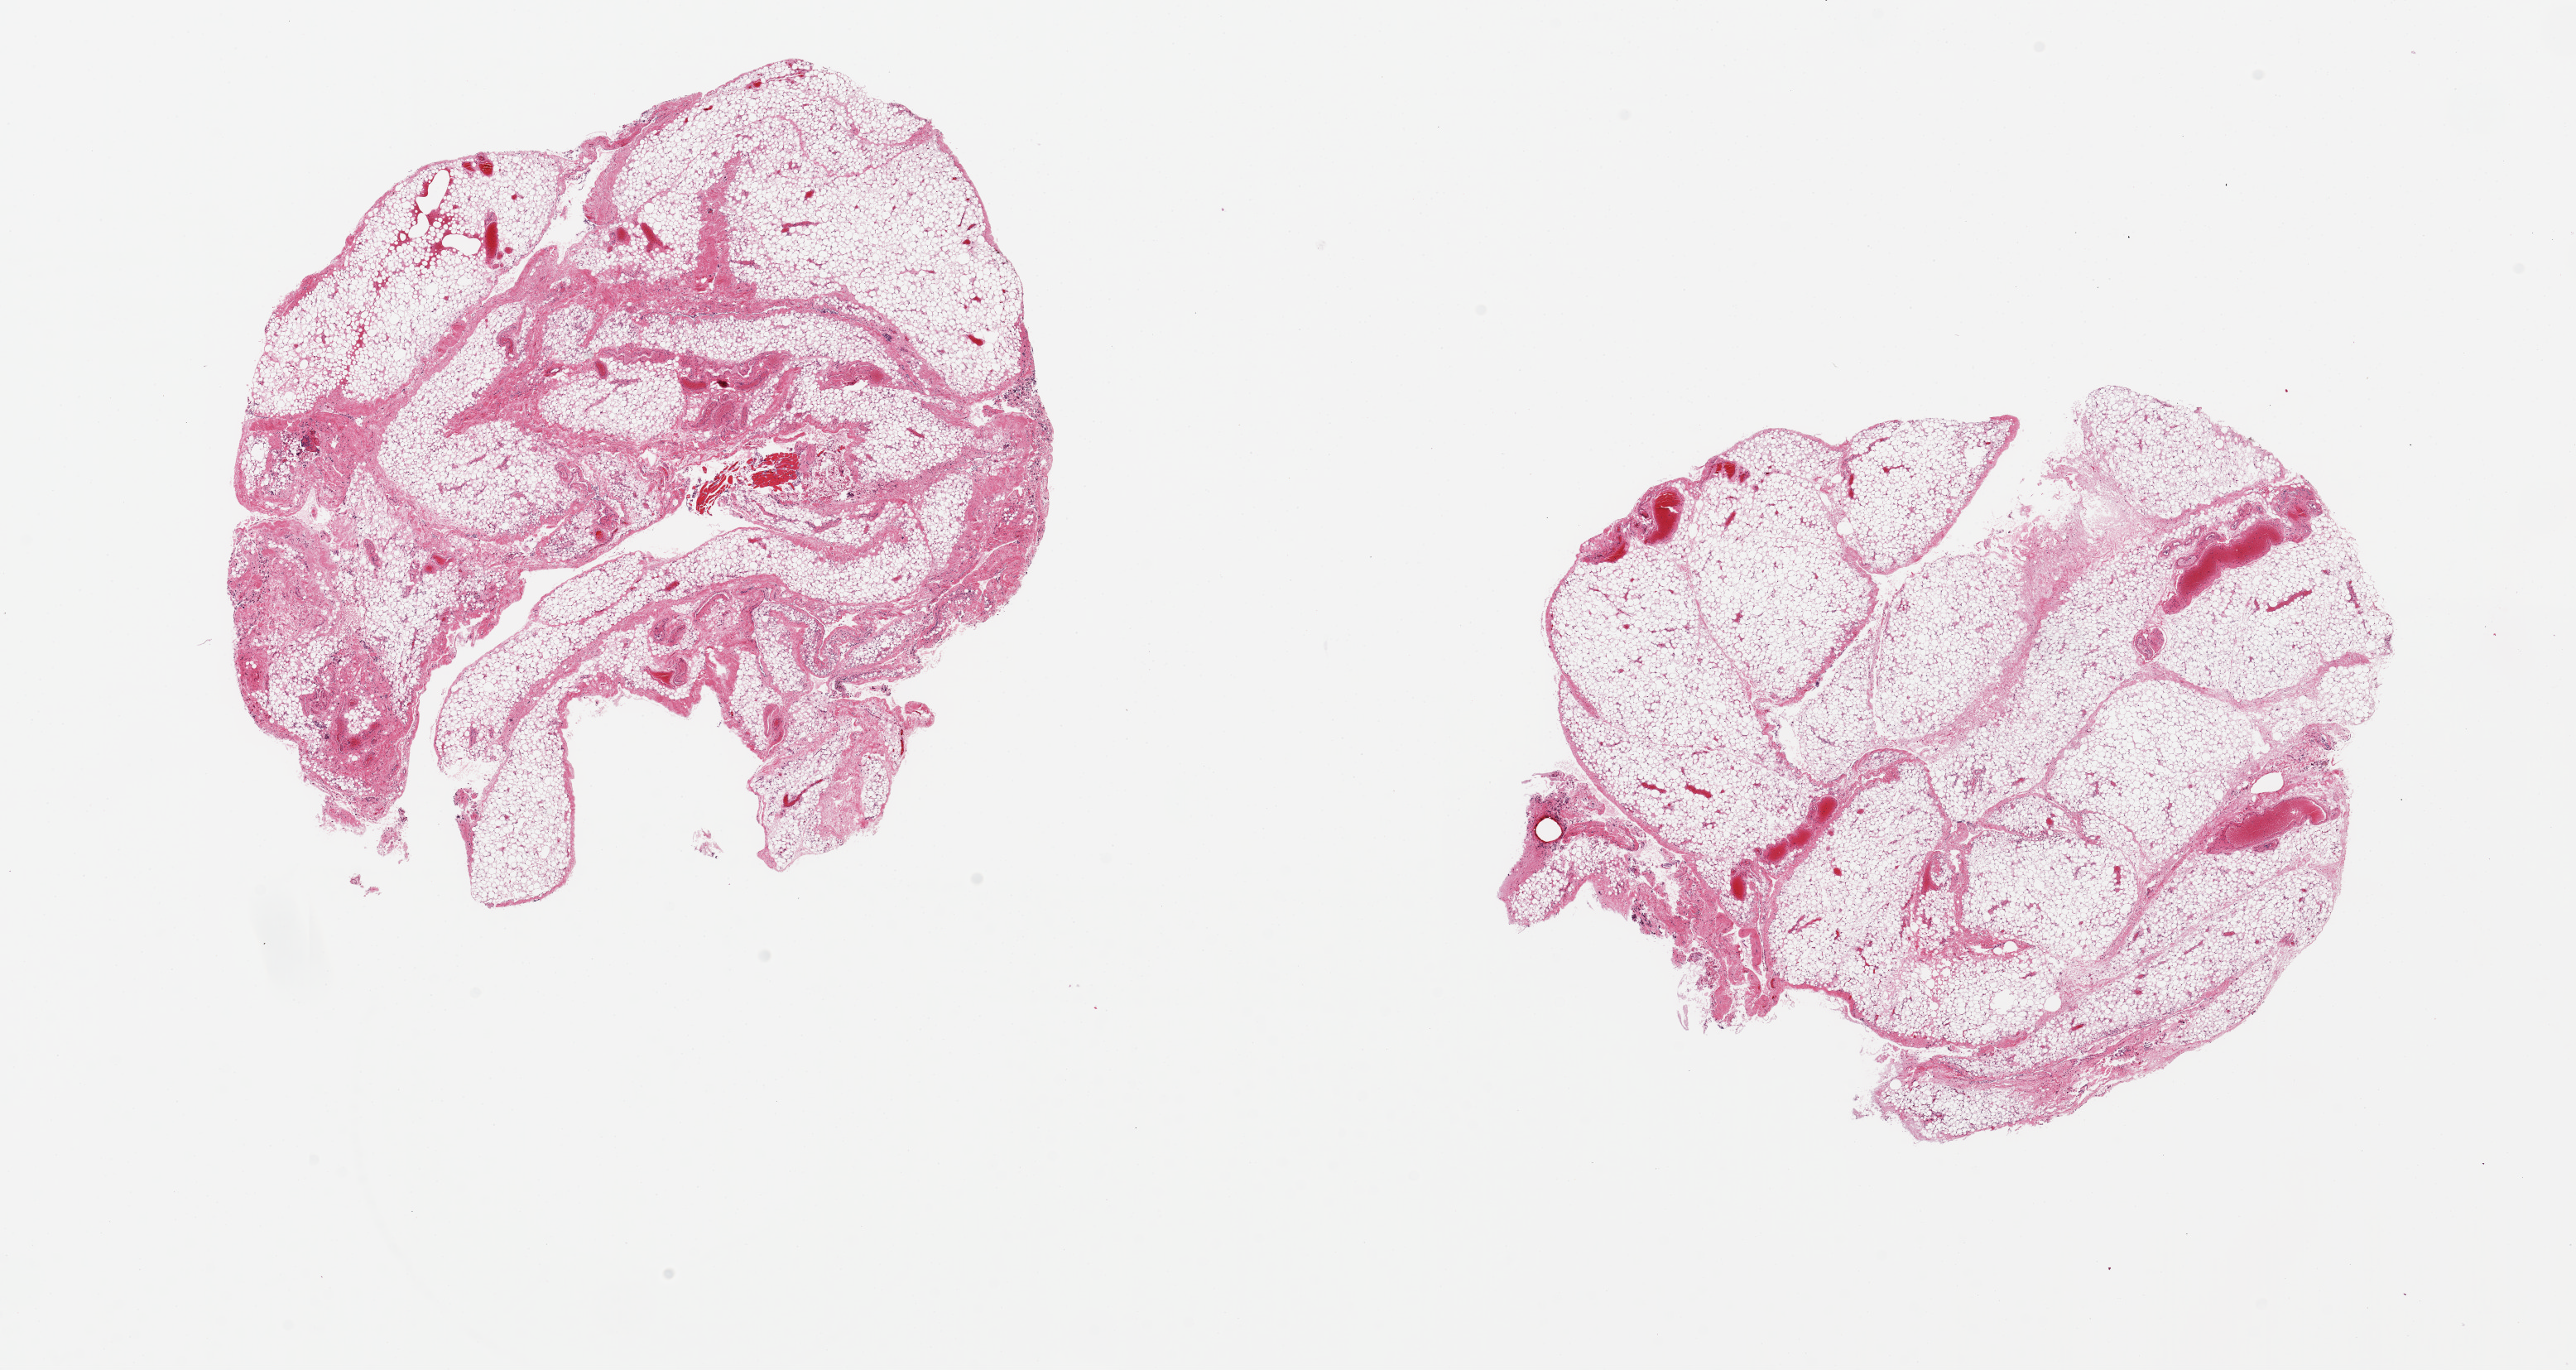
H&E whole-slide image, low-resolution overview of the scanned area, about 24.6 x 13.1 mm; PAXgene-fixed paraffin-embedded (PFPE) section; section of omentum (target tissue); donor tissue sample. Donor: male.
Reviewer comment on this tissue sample: 2 pieces 8x8 & 9x7mm.